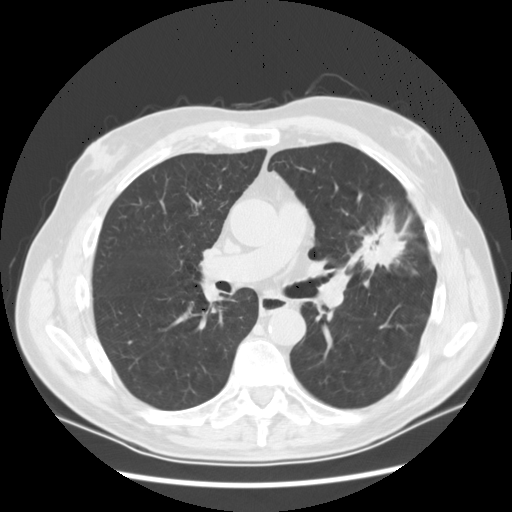
Axial slice from a low-dose chest CT screening exam. First (baseline) screen. Lung window (W 1500 / L -600 HU). Standard (soft-tissue) reconstruction kernel (STANDARD). 512 × 512 image matrix. Male, age 65 years at enrolment. Current smoker at enrolment.
Lesion marked by an expert reader, bounding box [x1, y1, x2, y2] px = [349, 213, 415, 282]. The exam's reader record, not a measurement of the box and not confirmed to be the same lesion: non-calcified nodule or mass ≥4 mm, left upper lobe, 37 × 27 mm, spiculated (stellate) margins, soft tissue attenuation. Official screen result: positive, change unspecified: nodule(s) >= 4 mm or enlarging nodule(s), mass(es), or other non-specific abnormalities suspicious for lung cancer. Lung cancer was diagnosed 56 days after this screen: non-small cell carcinoma, poorly differentiated (G3), stage IA (AJCC 6th edition).